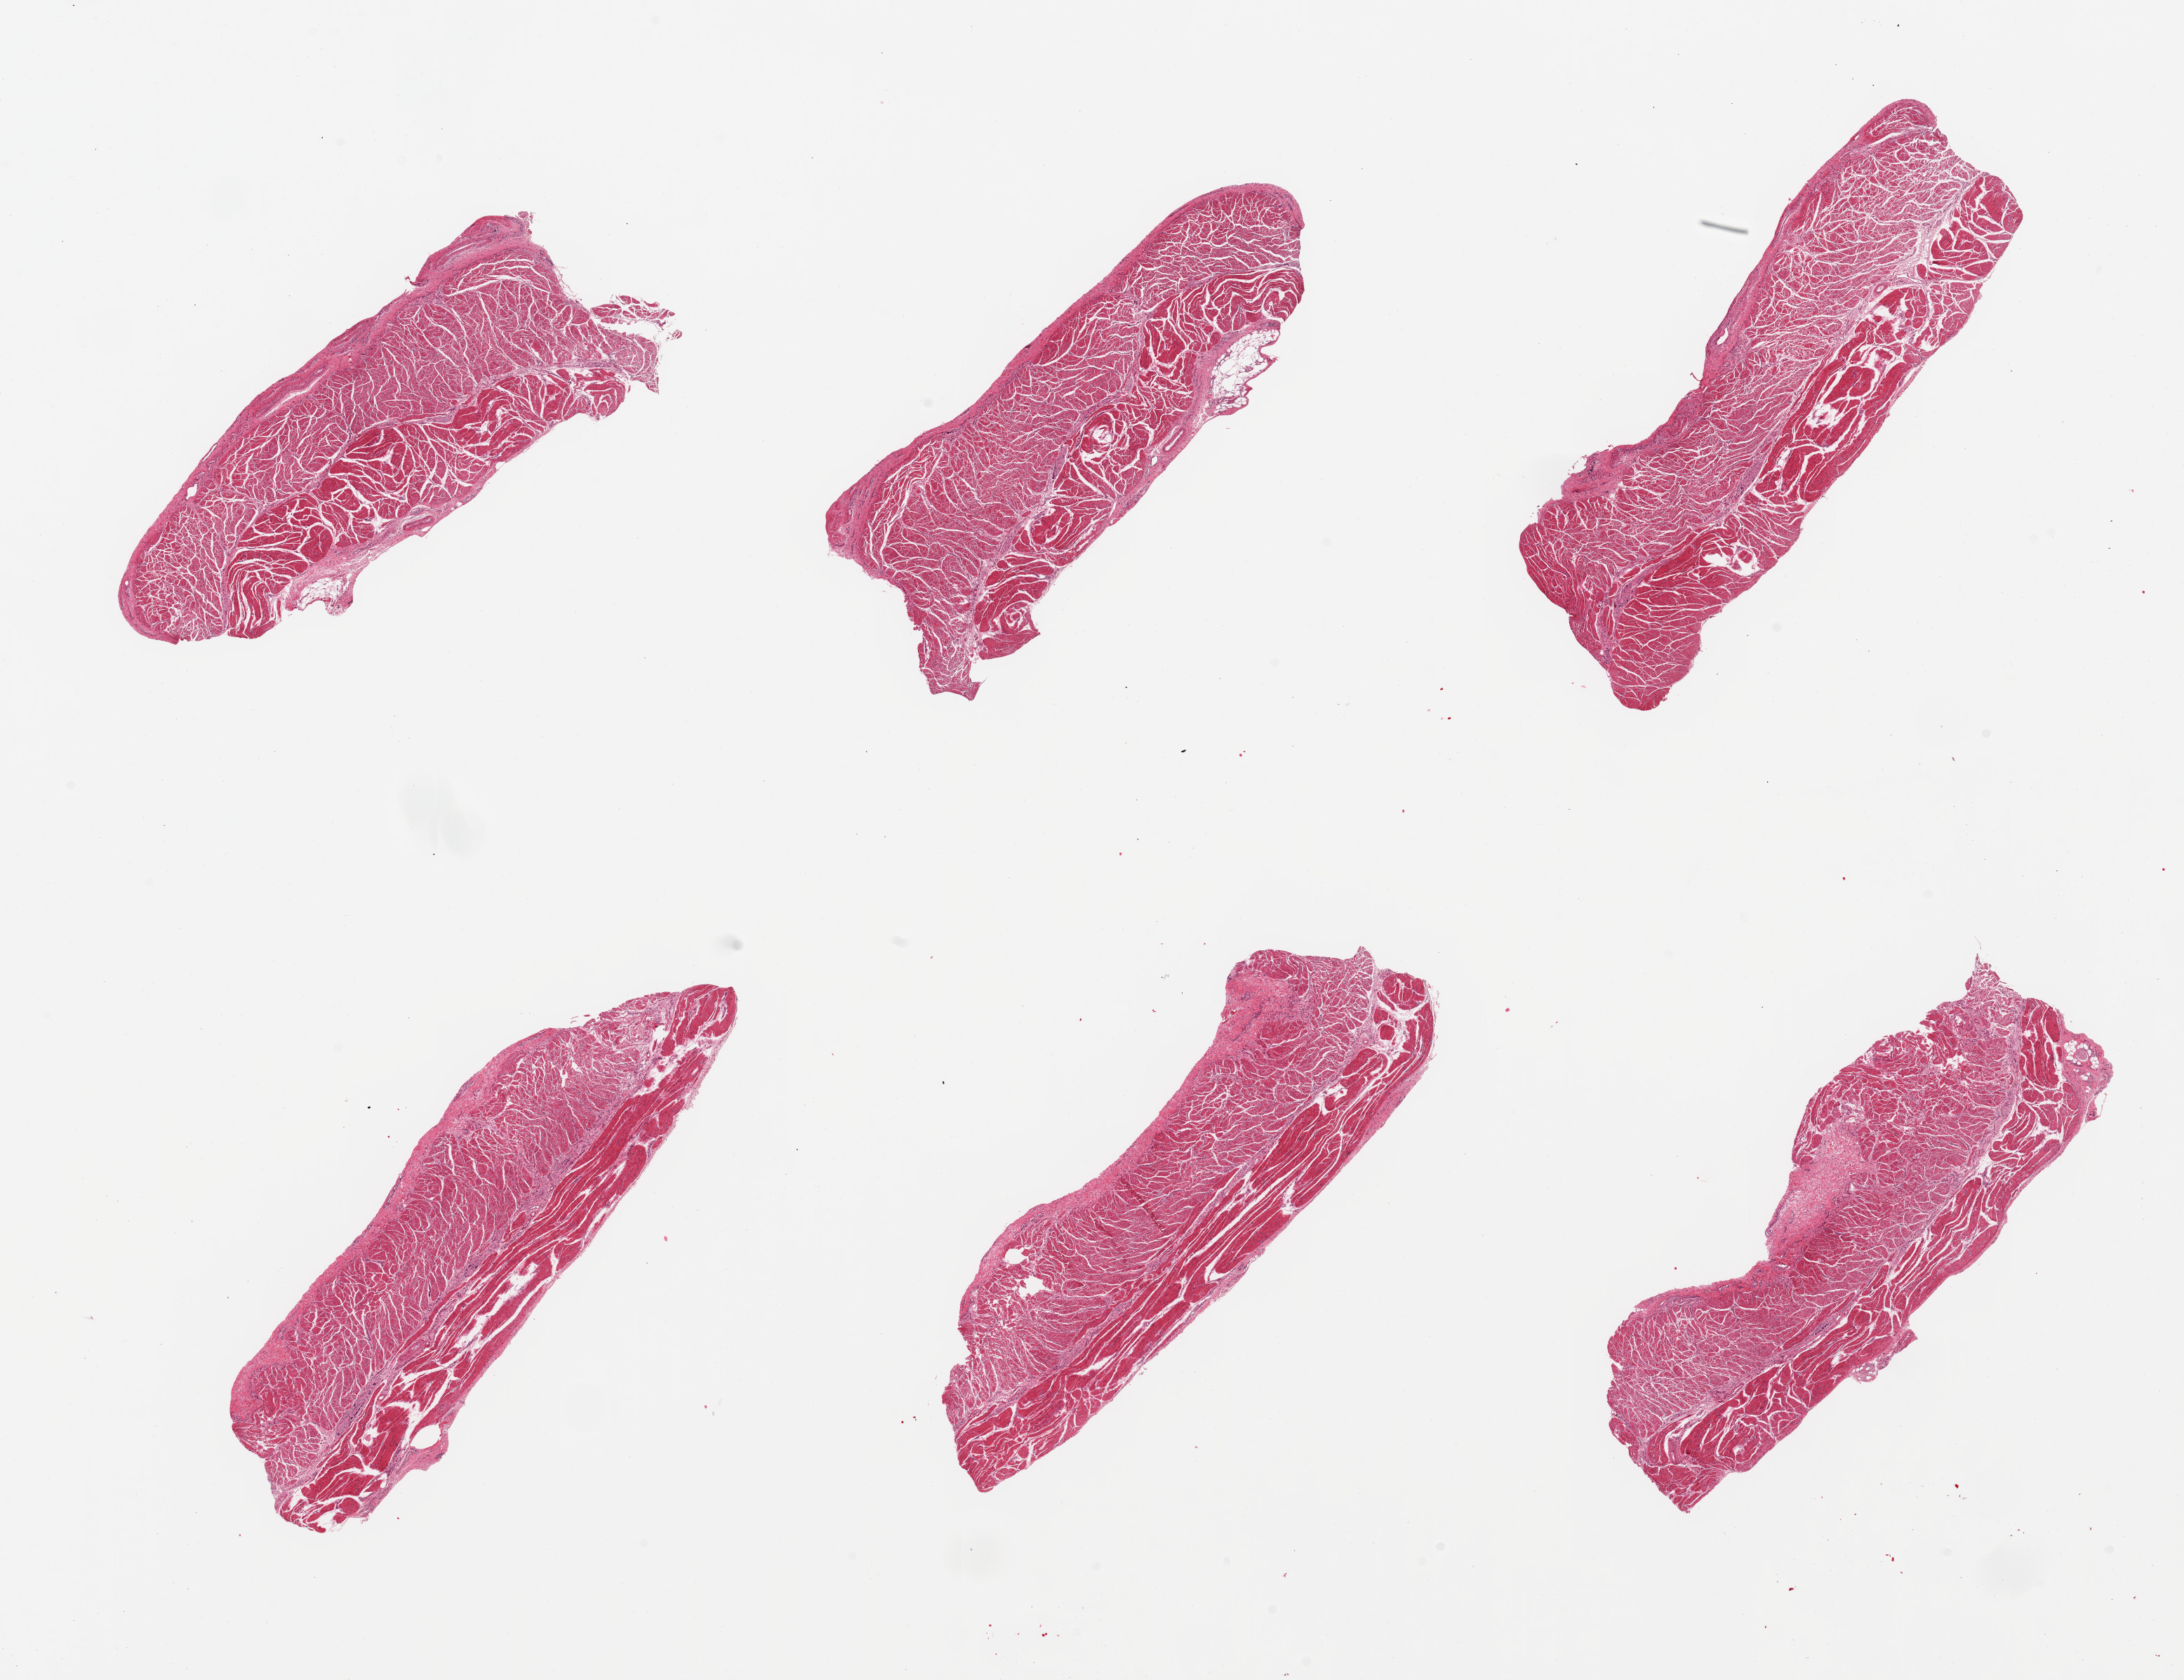
Digitized H&E-stained section, a low-resolution overview of the entire scanned area, about 24.6 x 18.9 mm, PAXgene-fixed paraffin-embedded (PFPE) section, target tissue: esophageal muscle, tissue donor sample. Donor sex: male.
* review note (as recorded): 6 pieces; well dissected